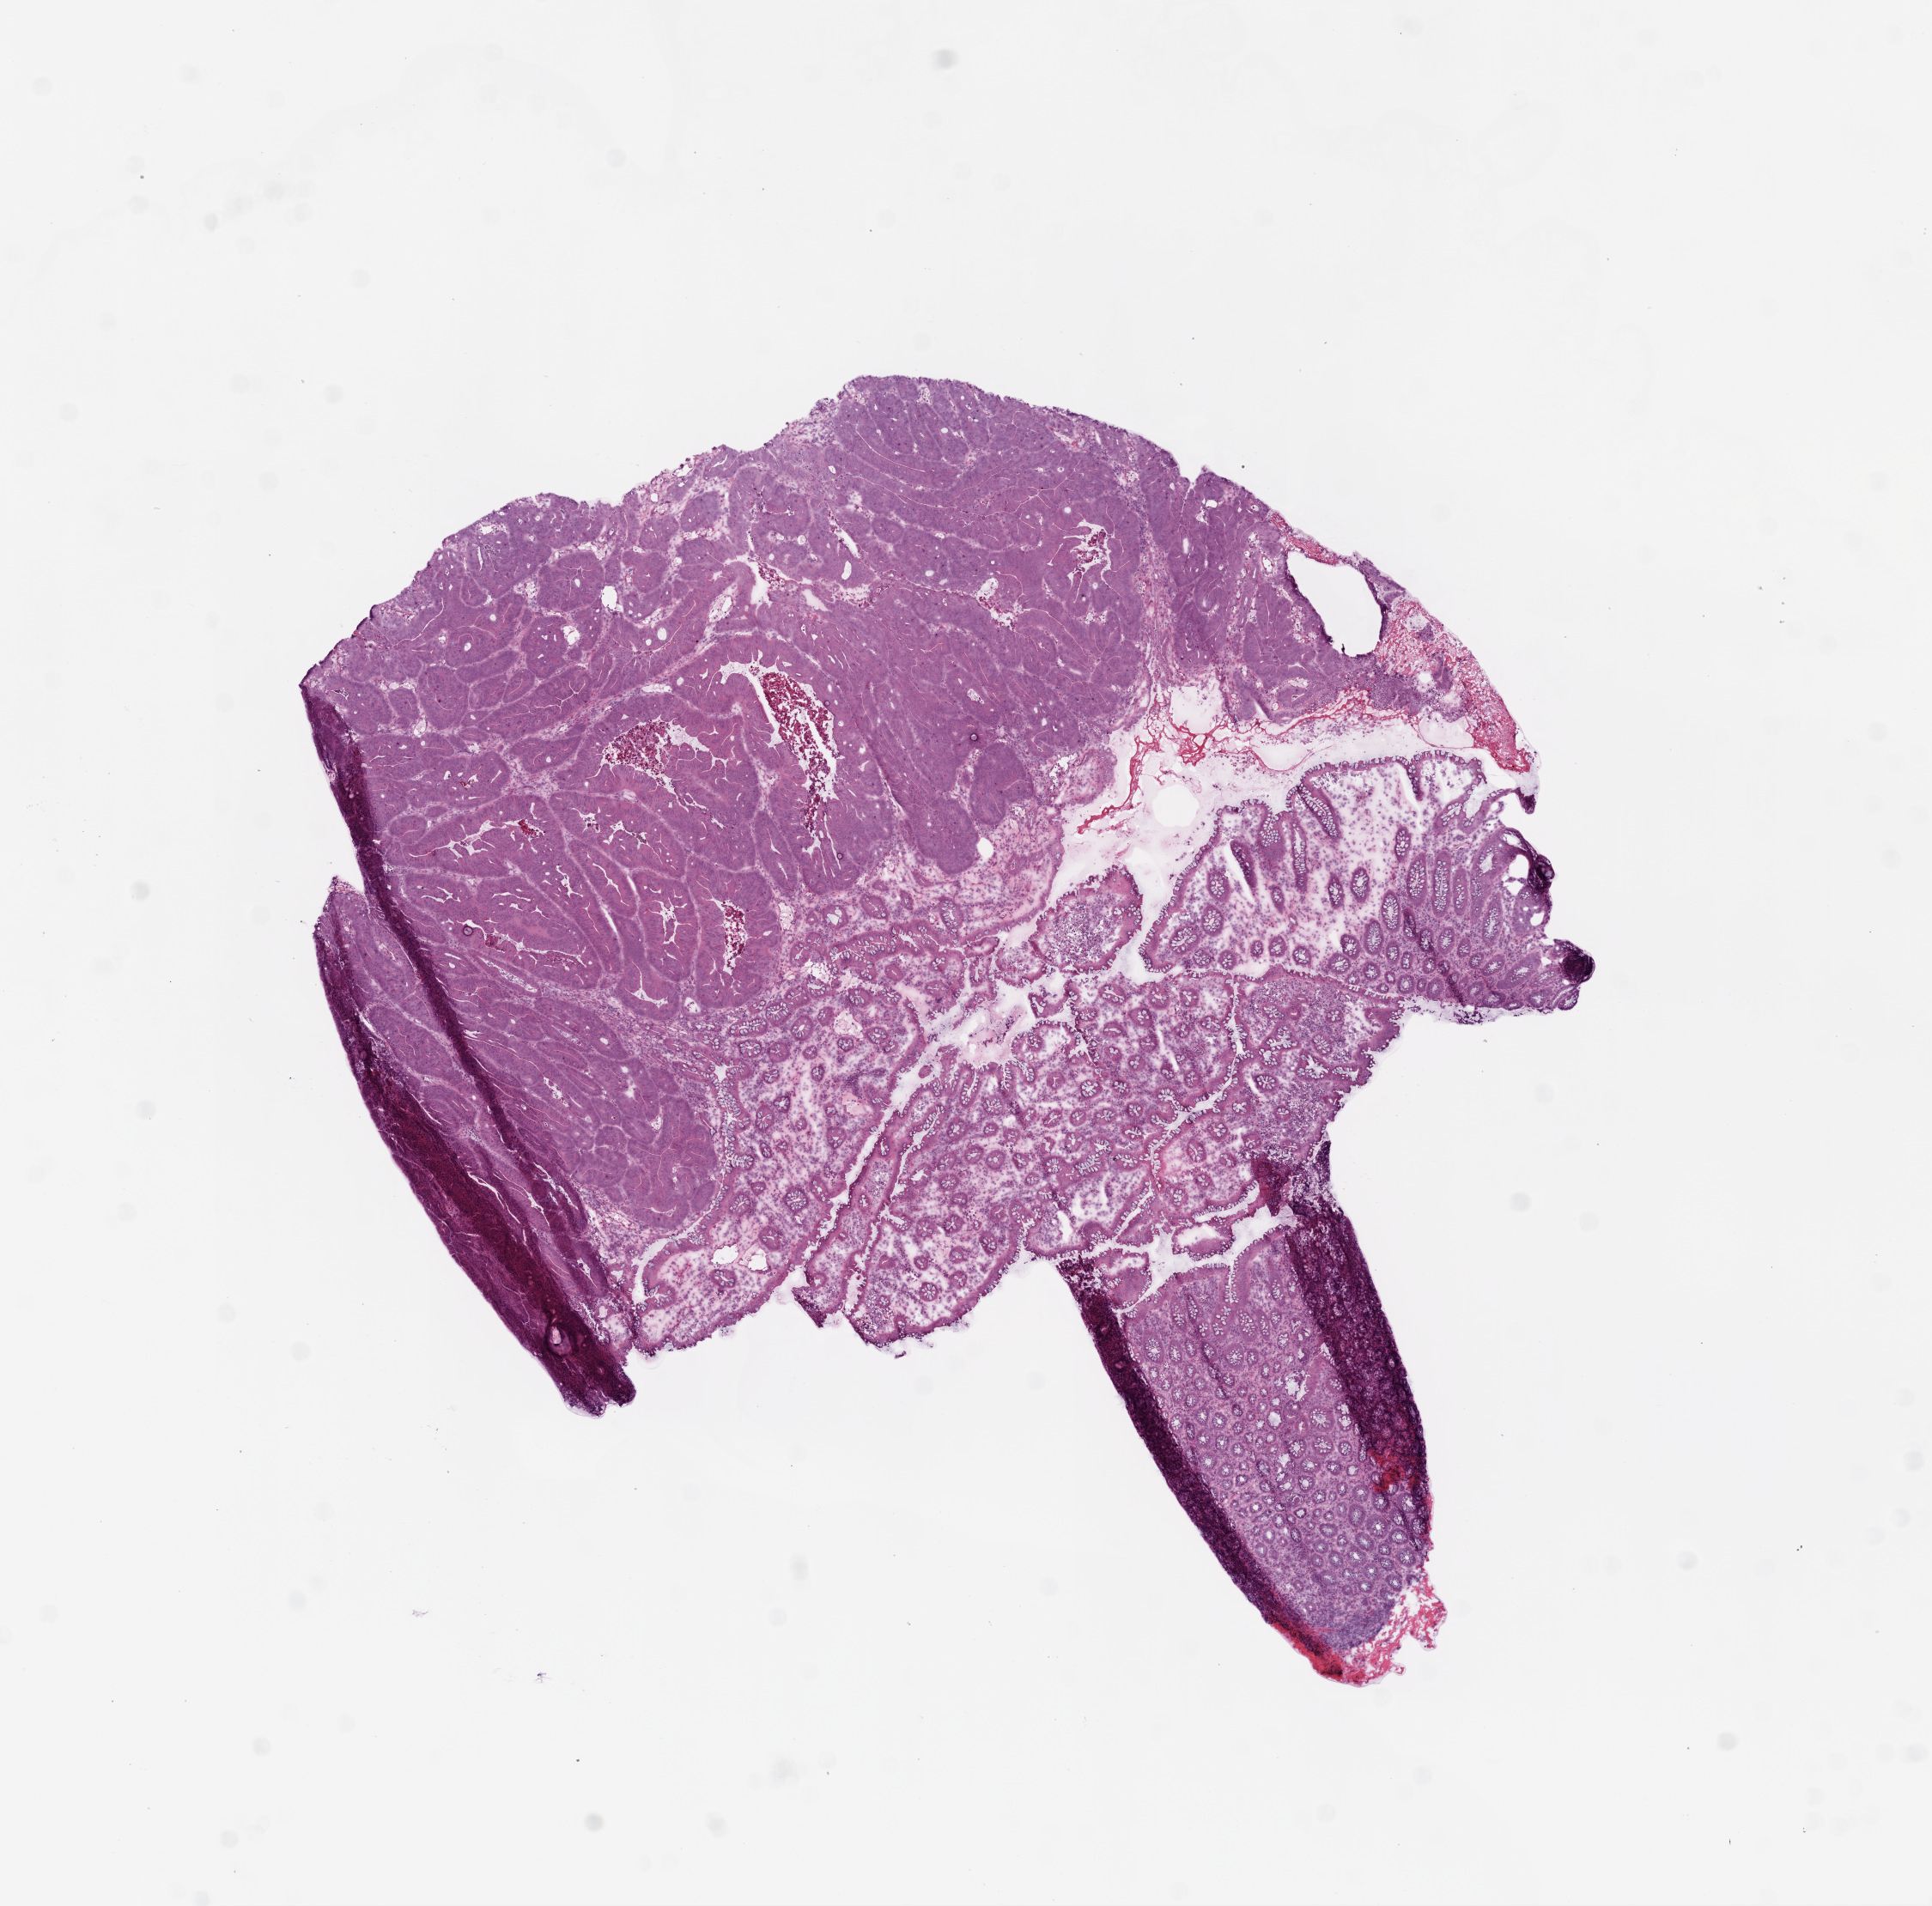
Whole-slide histology image, Hematoxylin and eosin (H&E) stained, low-resolution overview of the scanned area, about 9.0 x 8.9 mm, frozen section from the top of the tissue portion, primary tumour sample from the colon. Female, age 77 years at initial diagnosis. Composition of this section per pathologist review: tumour cells 55%, tumour nuclei 65%, normal cells 35%, stromal cells 5%, necrosis 5%.
Diagnosis: Adenocarcinoma, NOS (cecum). AJCC pathologic stage: III (5th edition). Lymph nodes positive (case pathology): 2 of 16 examined.